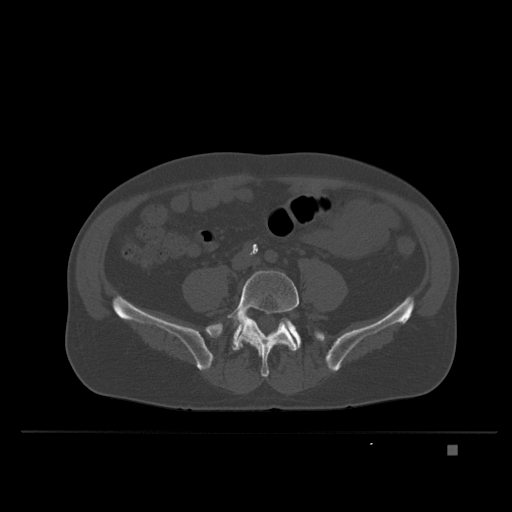
CT including the spine, one axial slice. Slice 56 of 435 in the series (ordered by position). Bone window (W 1800 / L 400 HU). 1.5 mm slice thickness. 512 × 512 image matrix, field of view 434 × 434 mm. Patient: male, 73 years. Case-level facts recorded for this patient, not image findings: primary cancer: skin.
Annotated regions visible in this slice (semi-automatic segmentation, software-assisted and operator-edited):
- L5 vertebra: box from (x=227, y=270) to (x=299, y=378) px